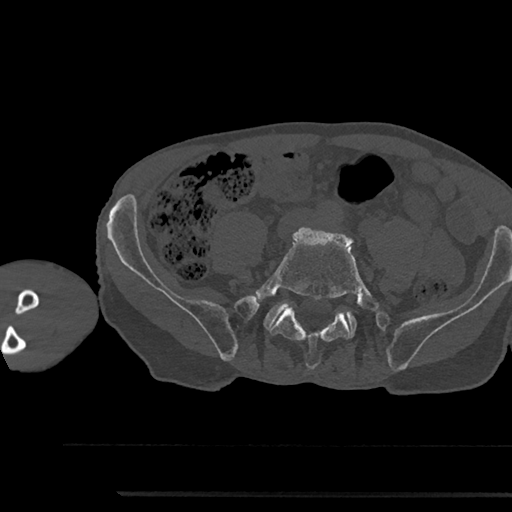
CT including the spine, one axial slice. Position 340 of 797 along the scan axis. 120 kVp. Bone window (W 1800 / L 400 HU). 0.5 mm slice thickness. 512 × 512 image matrix, field of view 367 × 367 mm. Male patient, age 79 years. From the clinical record (not read from this slice): primary cancer: prostate.
Structures marked on this image (semi-automatic segmentation, software-assisted and operator-edited):
- L5 vertebra: bounding box (x1, y1, x2, y2) in pixels: (253, 227, 380, 369)